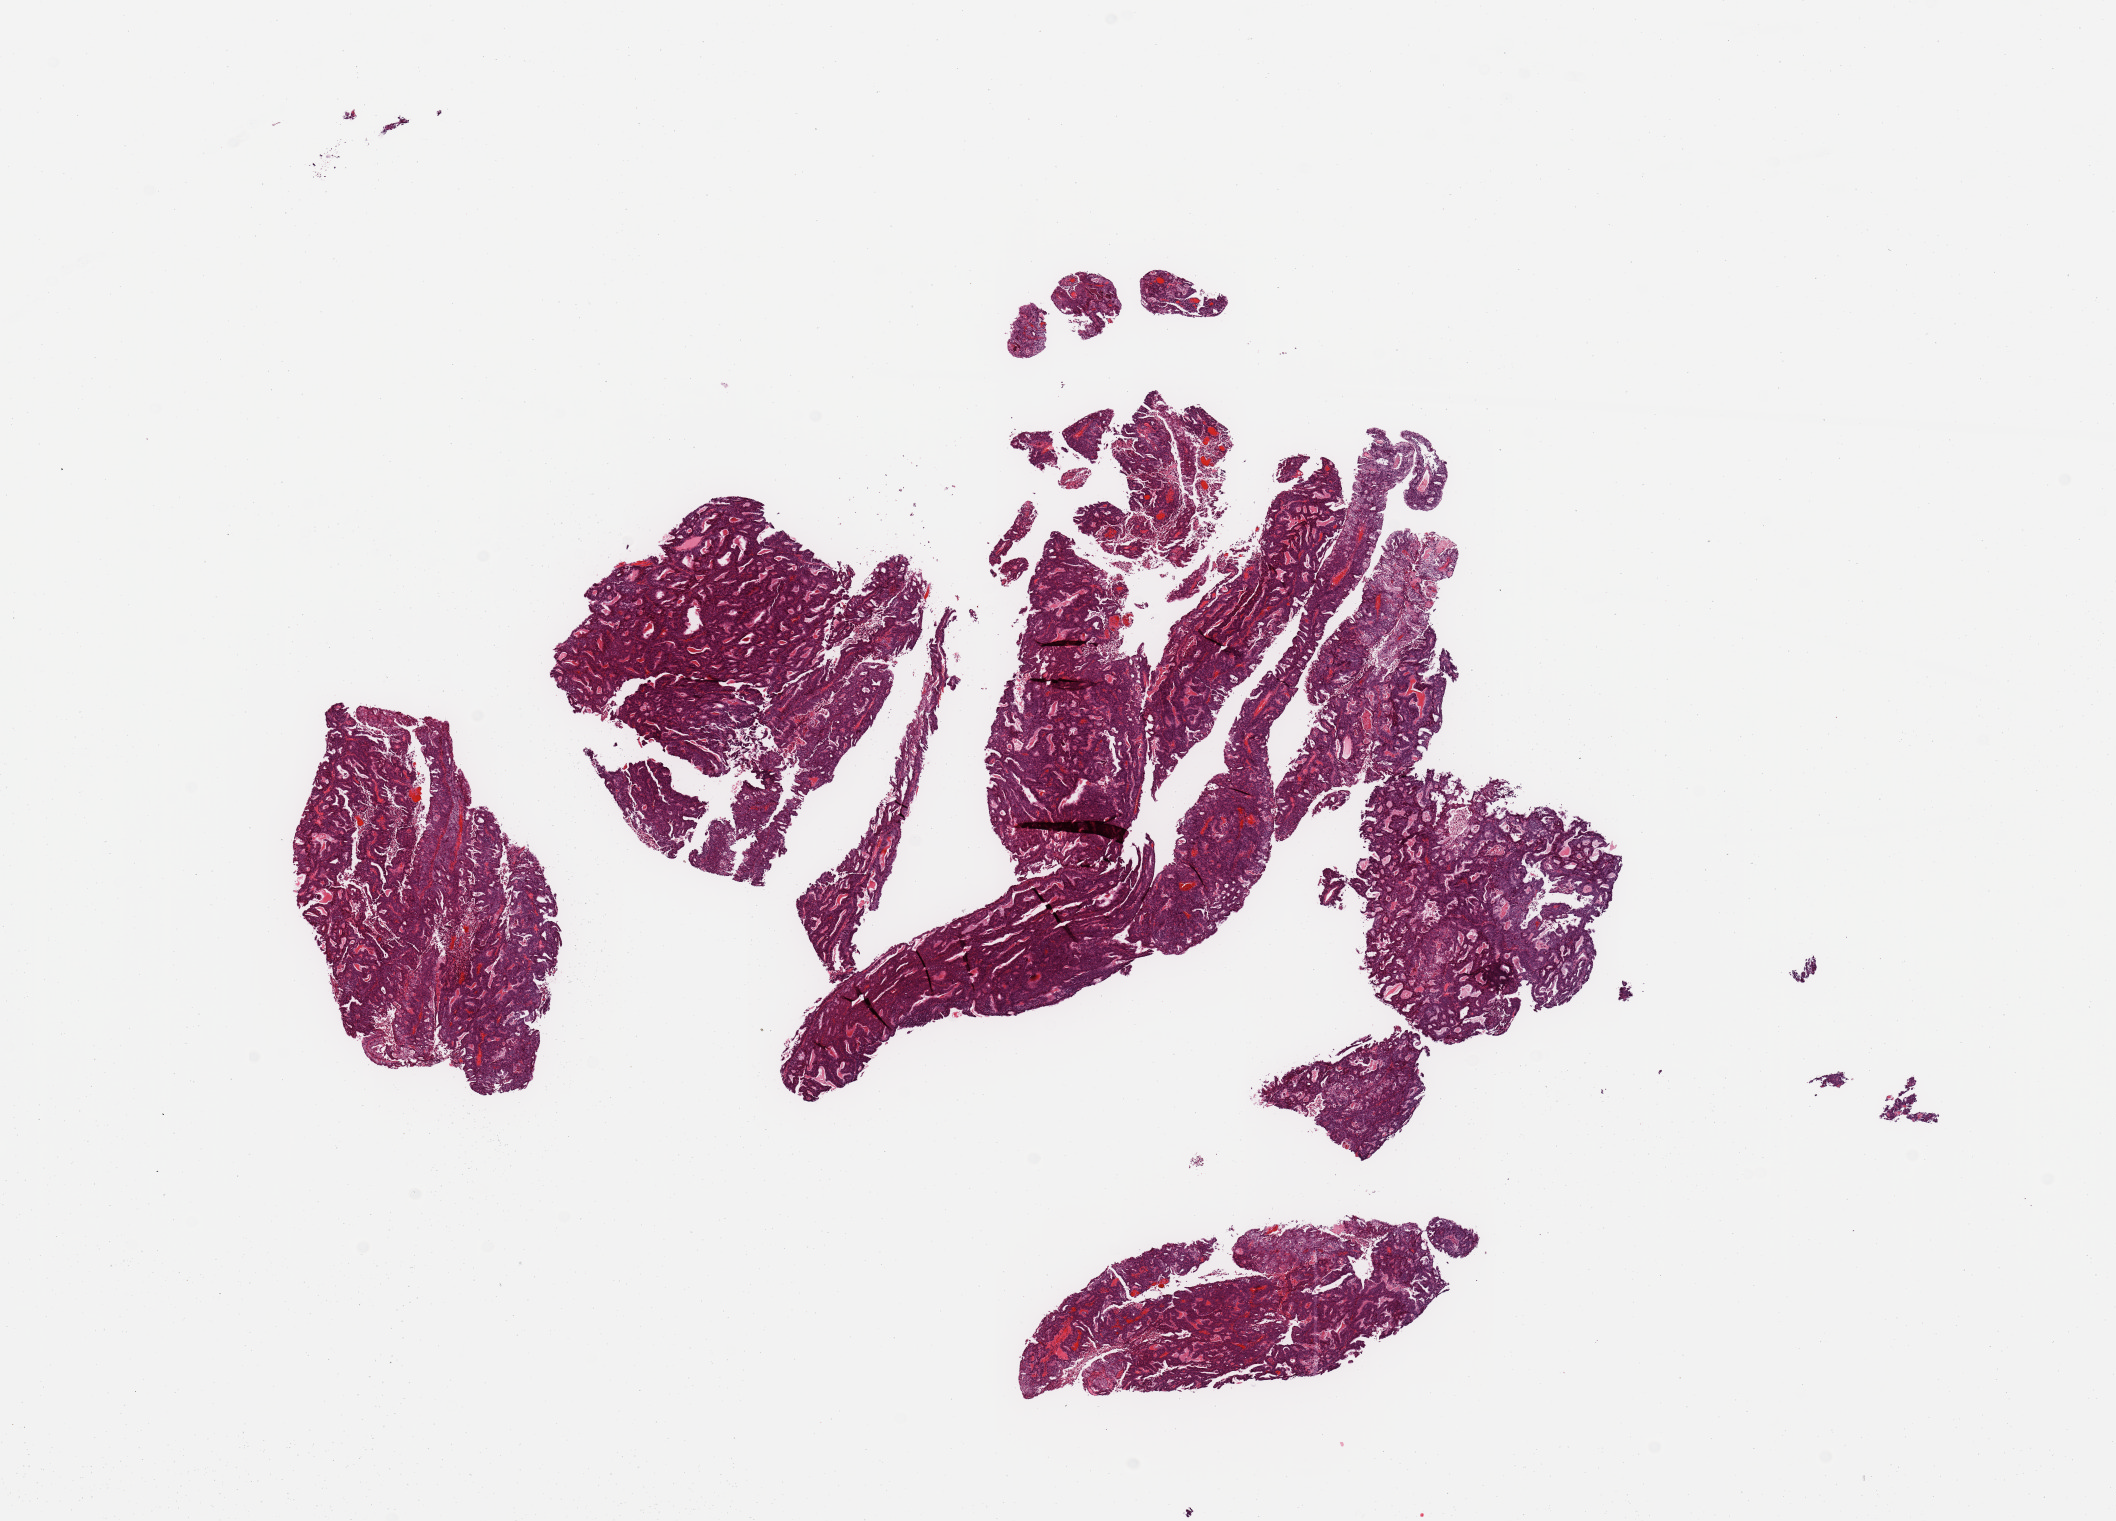
Whole-slide histology image, Hematoxylin and eosin (H&E) stained — whole scanned area (about 16.7 x 12.0 mm, slide scanned at 20x) shown as a low-resolution overview, tumour tissue sample, sampled site: uterus. Female, 55 y/o. Histologic grade: G1 (well differentiated). Pathologist review of this section (percent, as recorded): tumour nuclei 95%, necrosis 2%.
• histologic diagnosis: Endometrioid adenocarcinoma, NOS
• AJCC pathologic stage: III